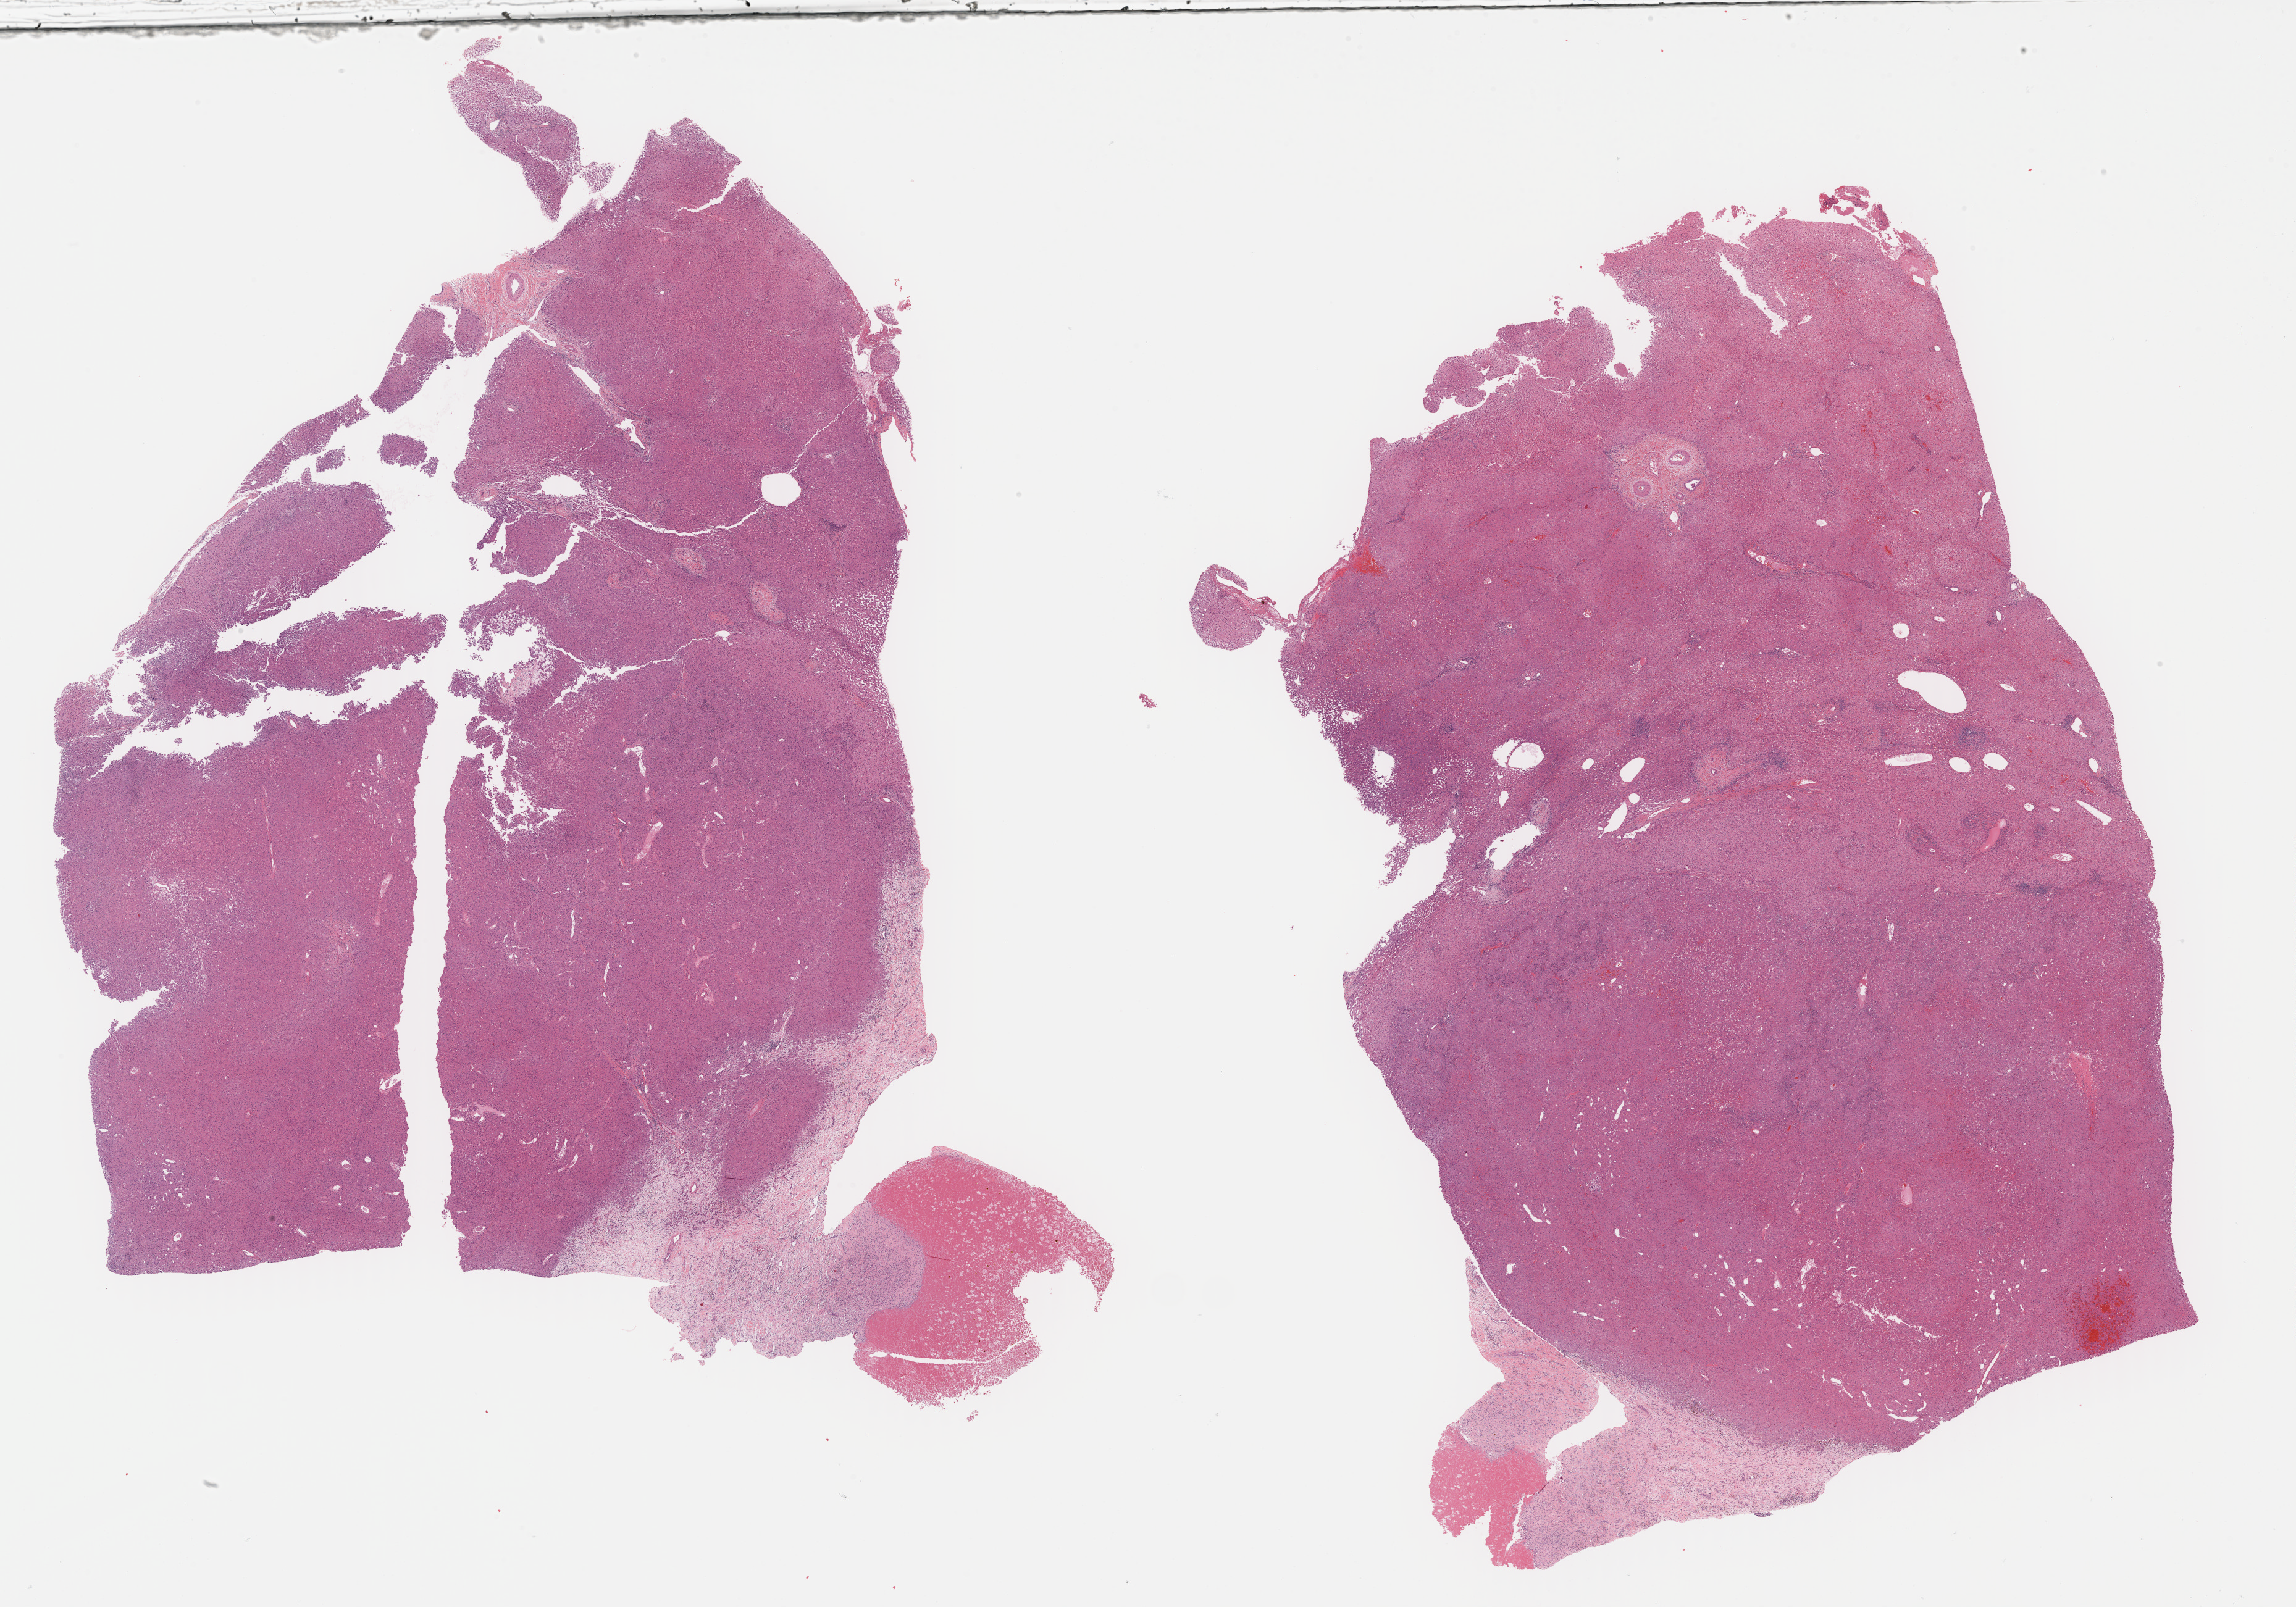
Whole-slide histology image, H&E-stained, shown as a low-resolution overview of the whole scanned area (about 30.1 x 21.1 mm). Formalin-fixed paraffin-embedded (FFPE) diagnostic section. Primary tumour sample from the liver. Male patient; age at initial diagnosis 46 years. Histologic grade: G1 (well differentiated).
• AJCC pathologic stage: I (6th edition)
• diagnosis: Hepatocellular carcinoma, NOS